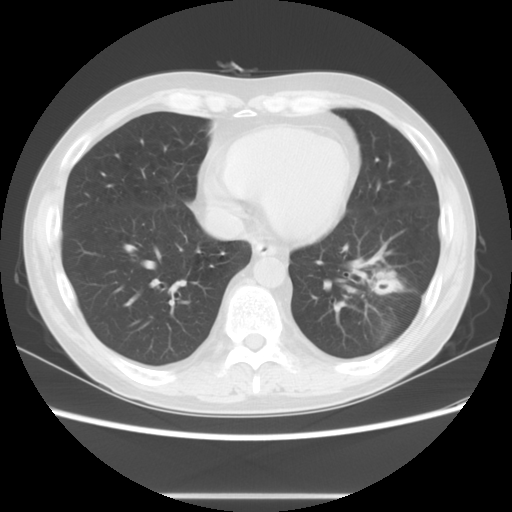
Chest CT, one axial slice; position 26 of 63 along the scan axis; reconstruction kernel STANDARD; 120 kVp; lung window (W 1500 / L -600 HU); 5 mm slice thickness; 512 × 512 image matrix. Patient: male, 49 years. Case-level facts recorded for this patient, not image findings: clinical TNM (as recorded): T3 N0 M0; histopathological grade: G2-3.
Outlined on this slice (bounding box drawn by a radiologist):
- lung tumour (recorded histology: squamous cell carcinoma): bounding box [x1, y1, x2, y2] px = [365, 260, 407, 301]